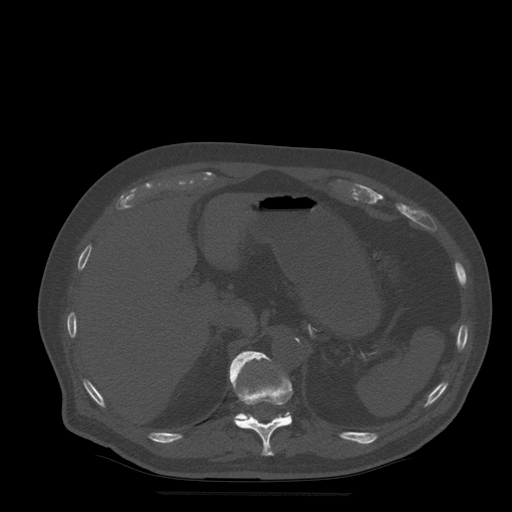
CT including the spine, one axial slice; slice 238 of 522 in the series (ordered by position); bone window (W 1800 / L 400 HU); 1.25 mm slice thickness; 512 × 512 image matrix, field of view 420 × 420 mm. Patient age 72 years. Case-level facts recorded for this patient, not image findings: primary cancer: prostate.
Outlined on this slice (semi-automatically segmented with operator editing):
- T11 vertebra: bounding box <233,353,293,456> (left, top, right, bottom; pixels)
- T12 vertebra: <230,351,290,420>